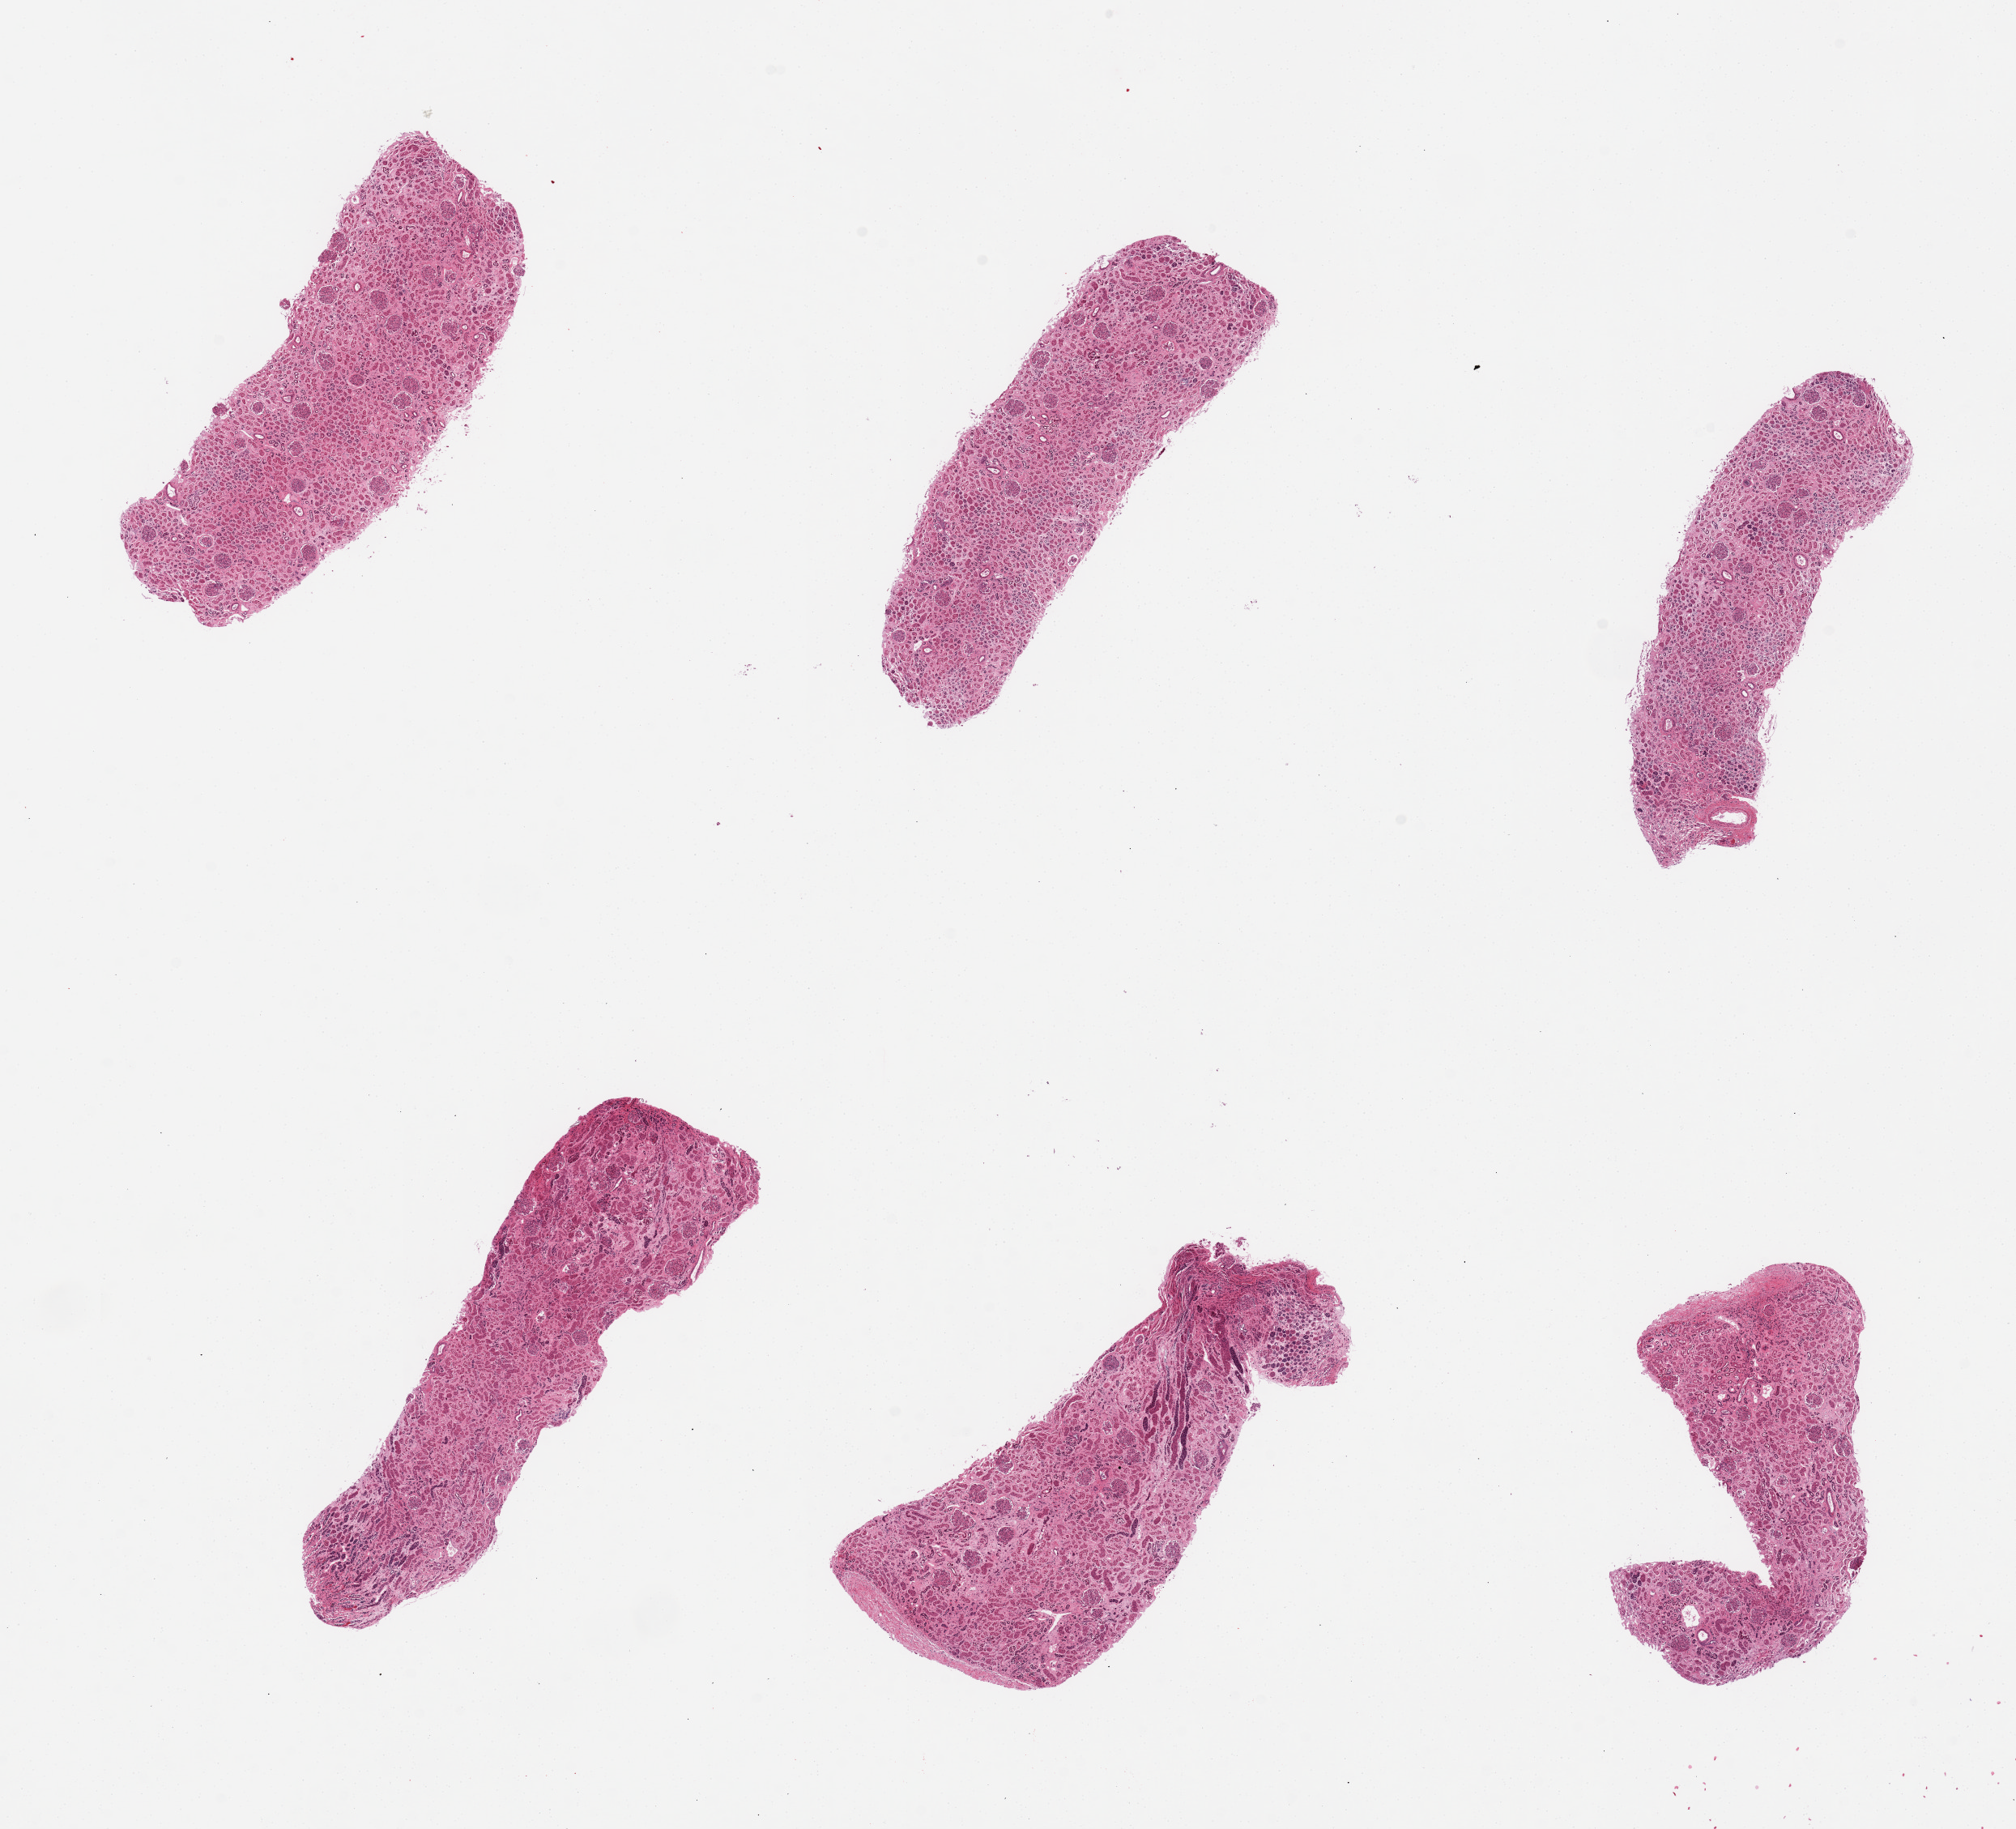
Digitized hematoxylin and eosin (H&E)-stained section, brightfield, whole scanned area (about 19.7 x 17.9 mm, from a 20x scan) shown as a low-resolution overview; PAXgene-fixed paraffin-embedded (PFPE) section; sampled site (target tissue): renal cortex; tissue donor sample. Donor sex: male.
Reviewer comment on this tissue sample: 6 pieces; tubules severely autolyzed.